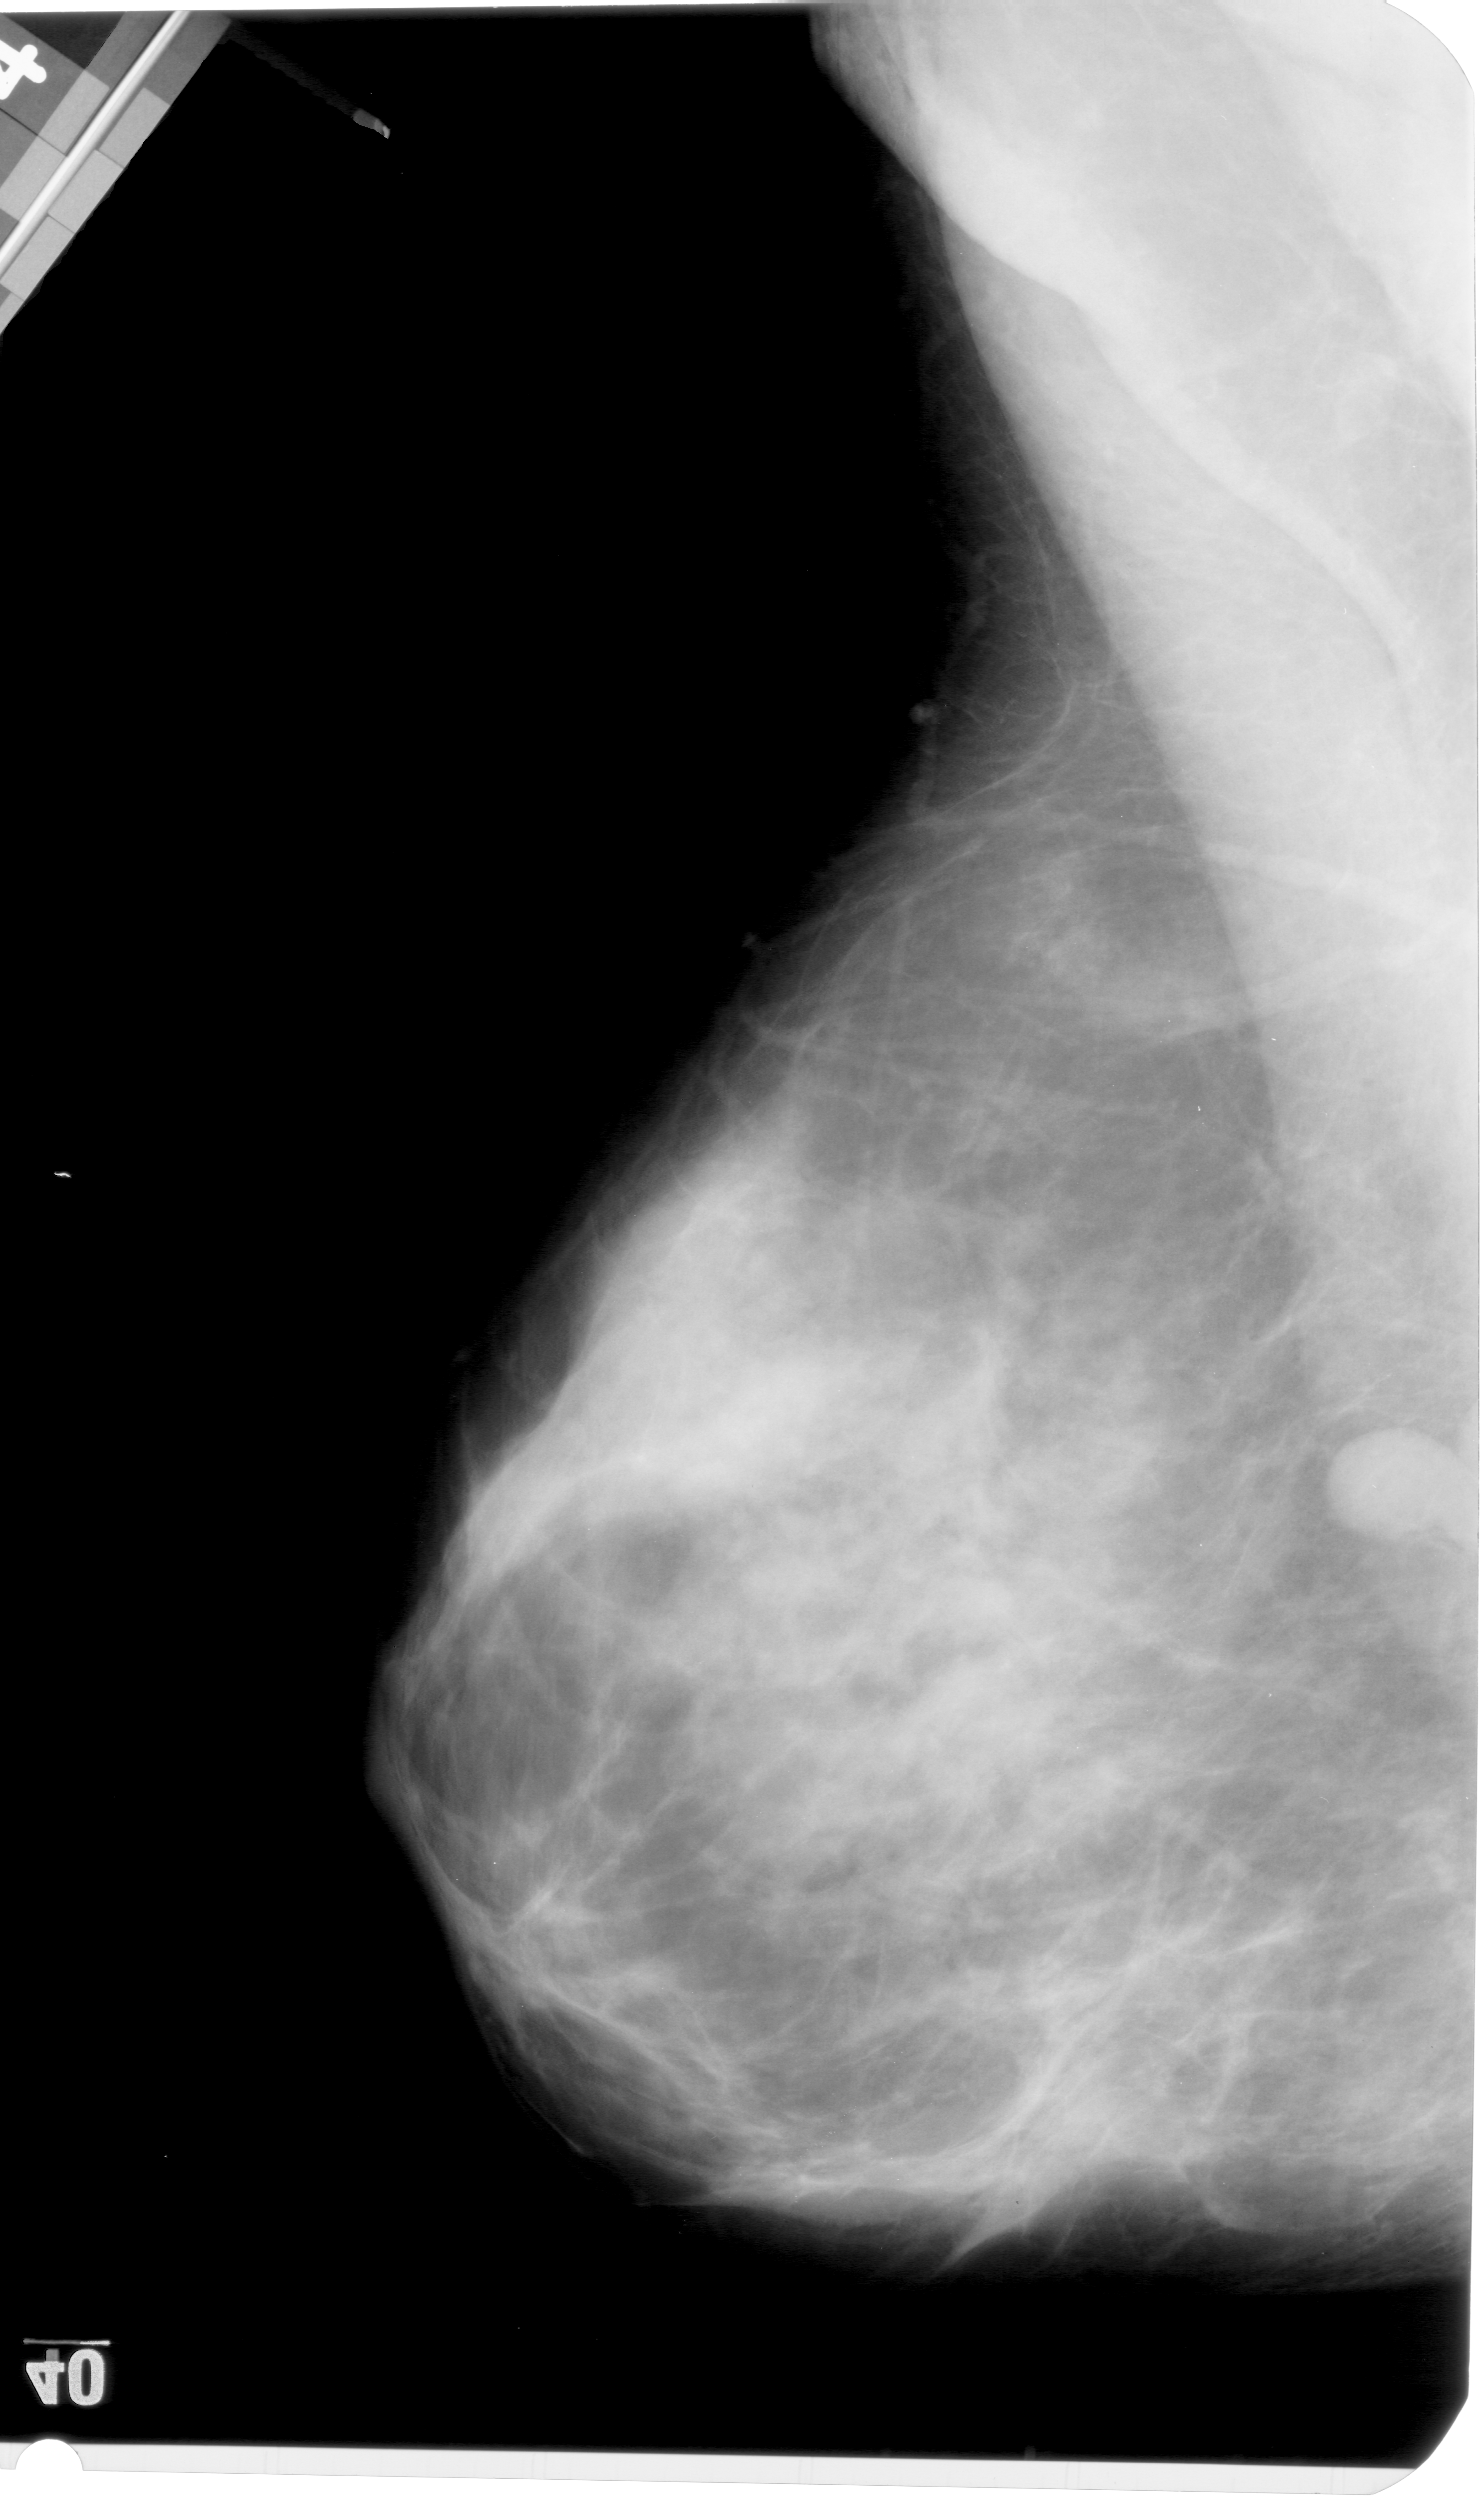
Digitized screen-film mammogram, left breast, mediolateral oblique (MLO) view.
Marked findings (only marked abnormalities are described; nothing is implied about the rest of the image): mass, shape lobulated, margins circumscribed; BI-RADS assessment category 4; pathology result (as recorded, not read from the image): benign.